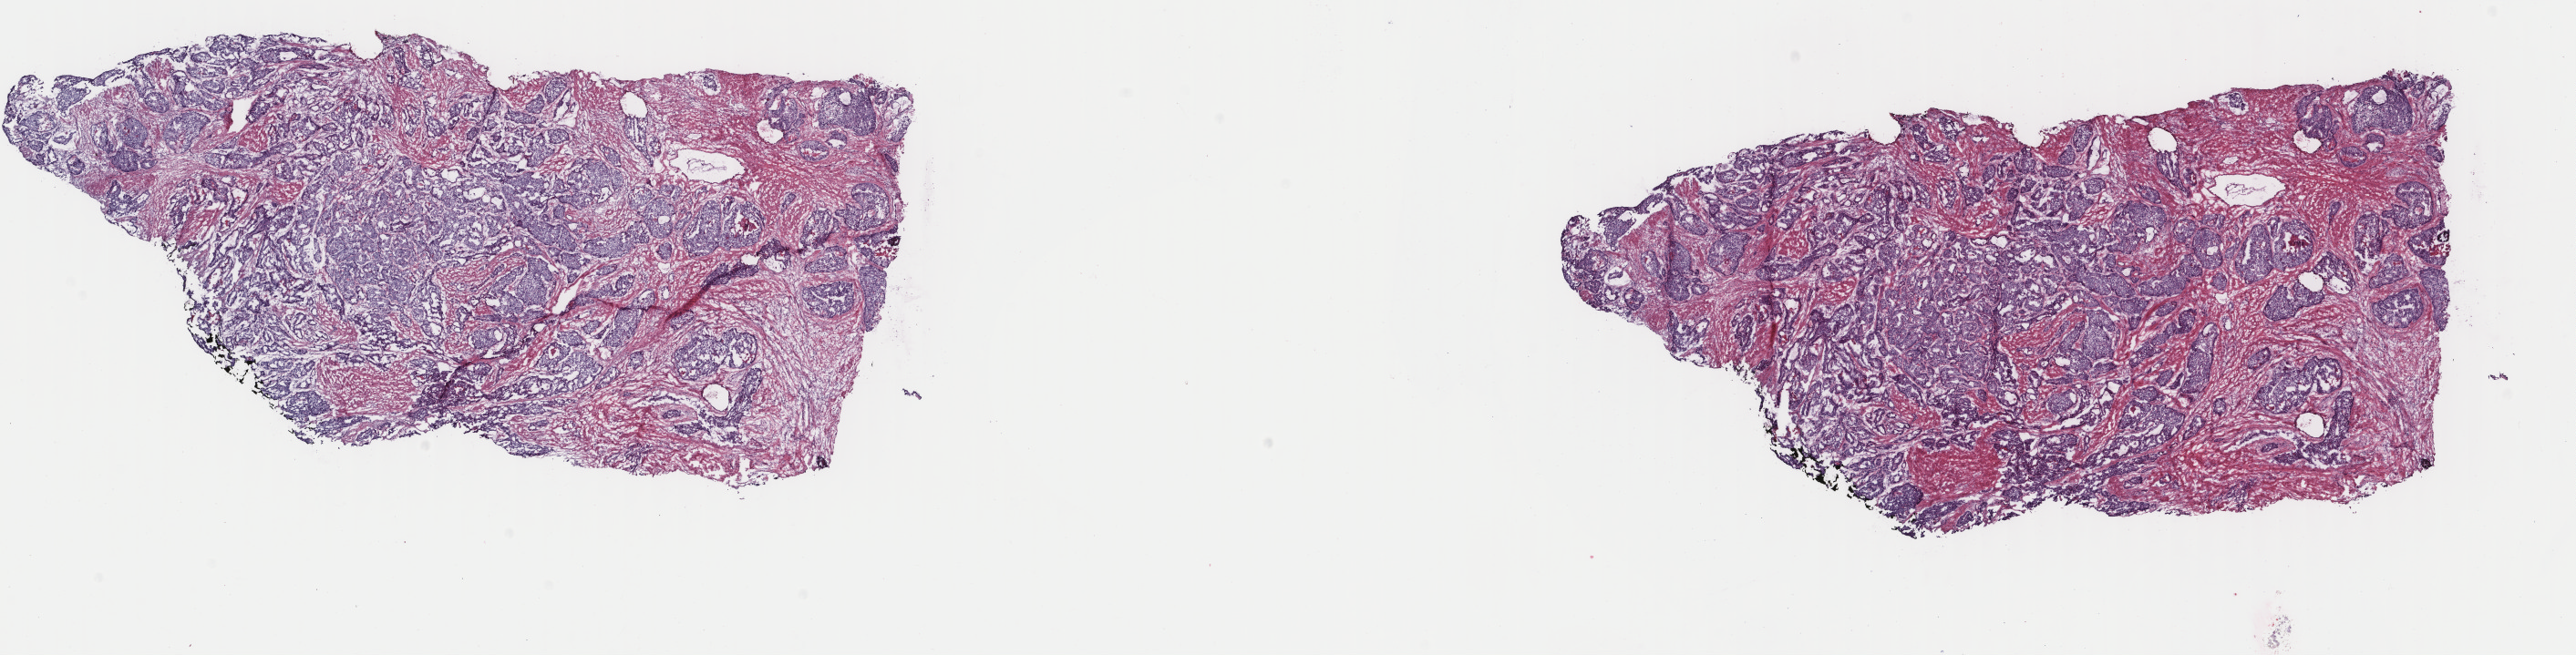
Digitized H&E tissue section (whole slide) — whole scanned area (about 22.4 x 5.7 mm, from a 40x scan) shown as a low-resolution overview; frozen section from the top of the tissue portion; primary tumour sample from the prostate. Male patient; age at initial diagnosis 47 years. Gleason score: 8 (4+4). Pathologist review of this section (percent, as recorded): tumour cells 69%, tumour nuclei 100%, normal cells 0%, stromal cells 30%, necrosis 1%. Infiltration values recorded for this section: lymphocyte infiltration 2%, monocyte infiltration 1%, neutrophil infiltration 0%.
Laterality: bilateral. Diagnosis: Adenocarcinoma, NOS (prostate gland).